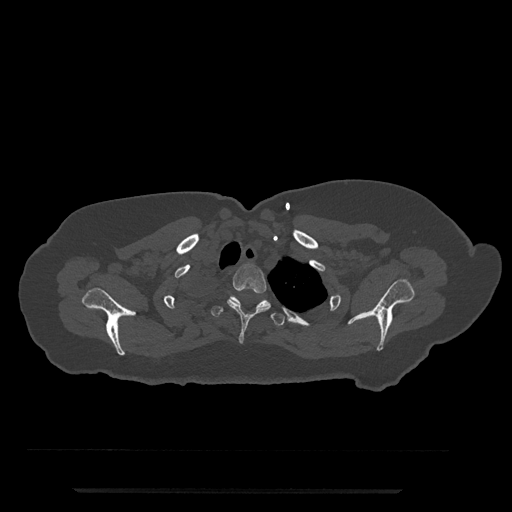
CT including the spine, one axial slice. Bone window (W 1800 / L 400 HU). 0.5 mm slice thickness. 512 × 512 image matrix, field of view 440 × 440 mm. Female patient, age 51 years. Case-level facts recorded for this patient, not image findings: primary cancer: neuro; vertebrae with lytic lesions (as recorded): T8.
Structures marked on this image (semi-automatic segmentation, software-assisted and operator-edited):
- T2 vertebra: box from (x=227, y=263) to (x=293, y=343) px
- T3 vertebra: (x=211, y=295)–(x=284, y=327)